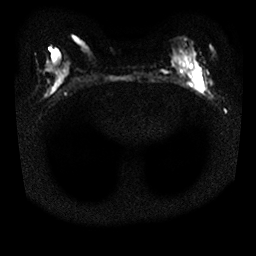
Breast MRI, one axial slice. Position 12 of 25 along the scan axis. Diffusion-weighted series; image 2 of 4 stored at this slice position (different b-values; order by instance number). 1.5 T. 4 mm slice thickness. 256 × 256 image matrix, field of view 310 × 310 mm. Female patient.
Annotated regions visible in this slice (outlined manually by an expert reader):
- tumour on diffusion-weighted imaging: bounding box [x1, y1, x2, y2] px = [192, 70, 204, 93]